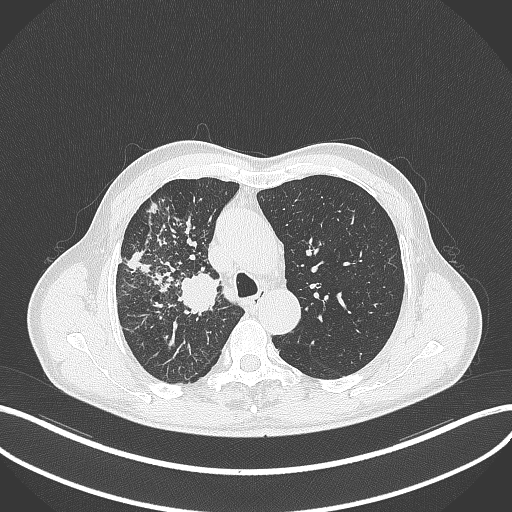
Chest CT, one axial slice. Slice 343 of 490 in the series (ordered by position). Reconstruction kernel B70f. 120 kVp. Lung window (W 1500 / L -600 HU). 512 × 512 image matrix, field of view 400 × 400 mm. Patient: male, 69 years. Case-level facts recorded for this patient, not image findings: clinical TNM (as recorded): T2a N0 M0.
Structures marked on this image (rectangle marked by the reading radiologist):
- lung tumour (recorded histology: adenocarcinoma): bounding box [x1, y1, x2, y2] px = [178, 268, 223, 319]